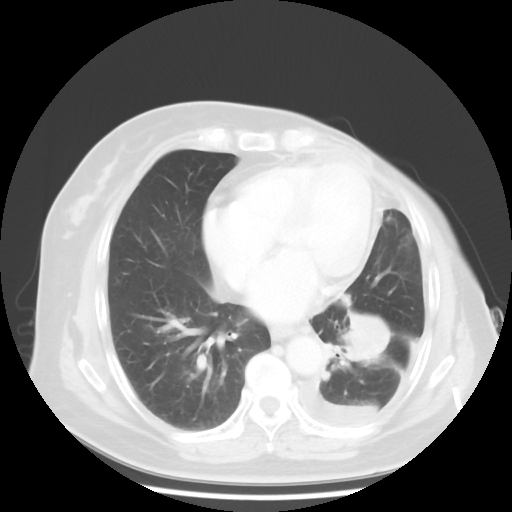
Chest CT, one axial slice; slice 17 of 48 in the series (ordered by position); lung window (W 1500 / L -600 HU); 5 mm slice thickness; 512 × 512 image matrix. Patient: female, 63 years. From the clinical record (not read from this slice): clinical TNM (as recorded): T2 N0 M1.
Annotated regions visible in this slice (bounding box drawn by a radiologist):
- lung tumour (recorded histology: adenocarcinoma): bounding box <330,295,416,383> (left, top, right, bottom; pixels)